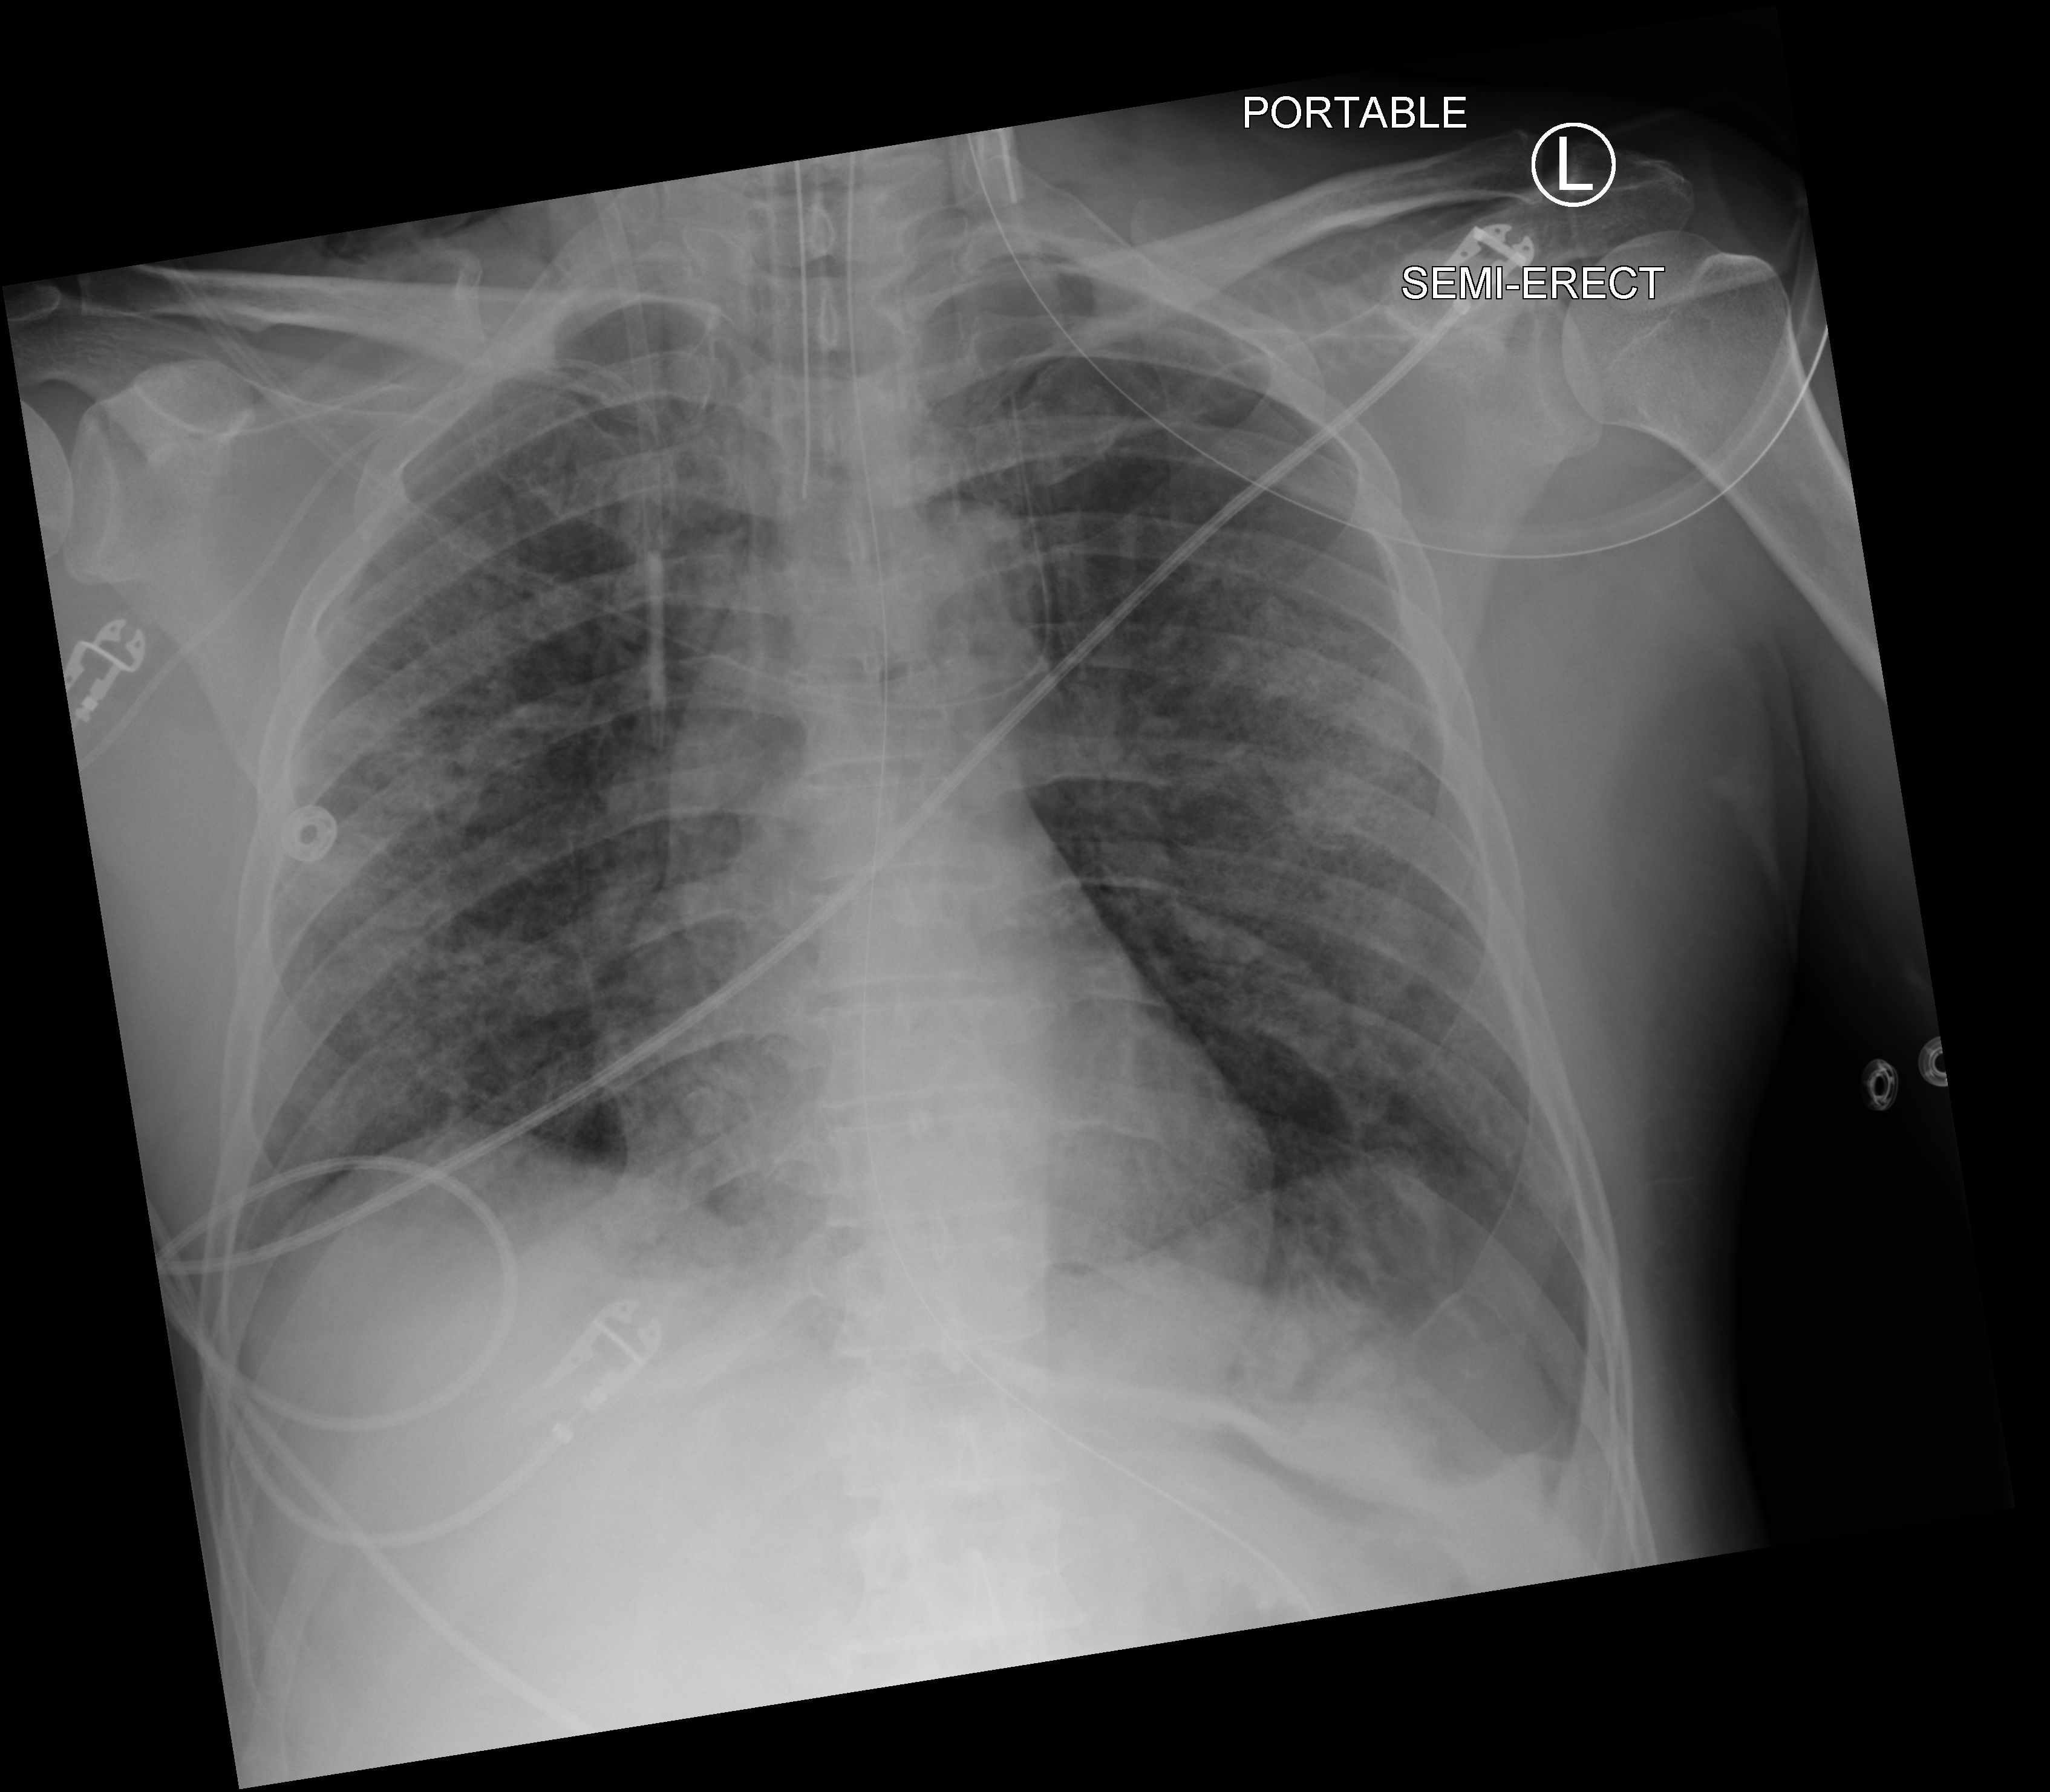
Portable chest radiograph, anteroposterior (AP) projection. Male patient hospitalised with COVID-19, age 18–59 years.
Admission-level facts for this patient (not findings on this image; timing relative to this image not recorded): diabetes (admission record): no; COPD (admission record): no.